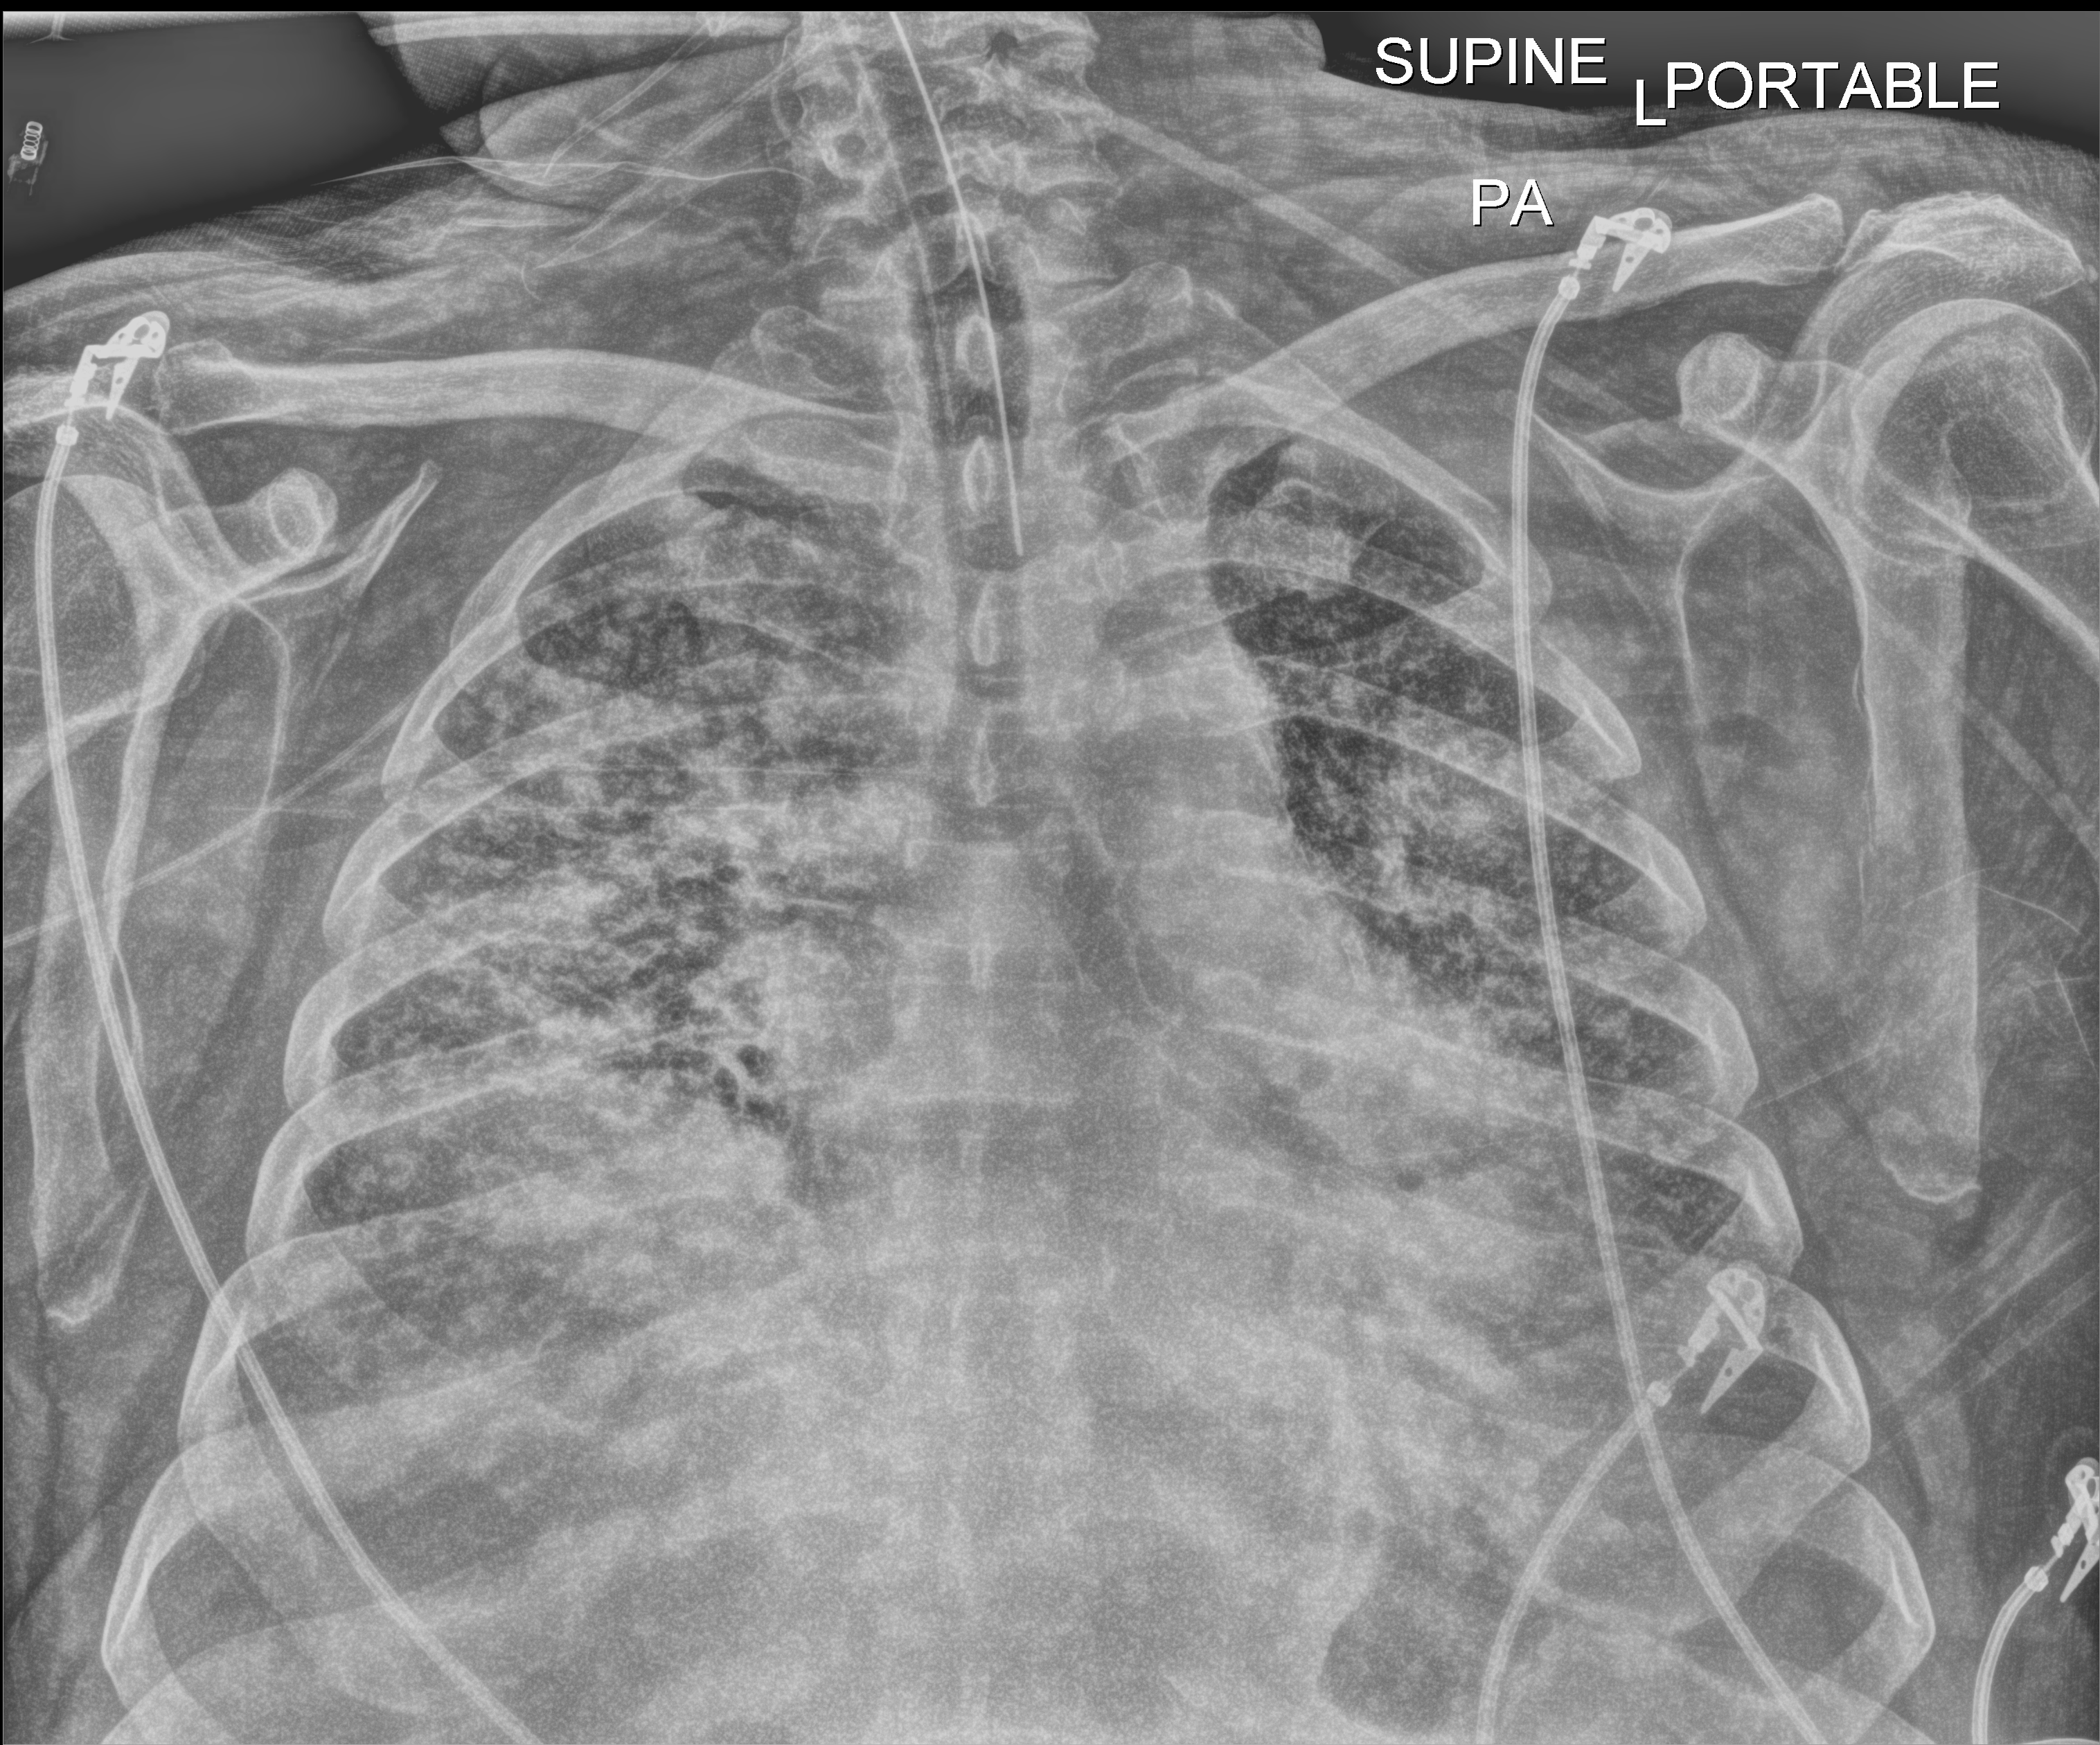
Chest X-ray (portable). Patient hospitalised with COVID-19; male, aged 60–74 years.
Admission-level facts for this patient (not findings on this image; timing relative to this image not recorded): mechanically ventilated during this hospital stay: yes; admitted to intensive care during this hospital stay: yes.